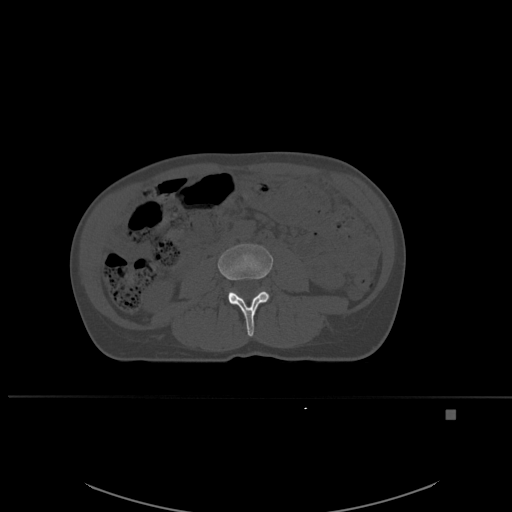
CT including the spine, one axial slice; slice 208 of 537 in the series (ordered by position); bone window (W 1800 / L 400 HU); 1.5 mm slice thickness; 512 × 512 image matrix, field of view 440 × 440 mm. Patient: female, 45 years. From the clinical record (not read from this slice): primary cancer: lung.
Annotated regions visible in this slice (semi-automatic segmentation, software-assisted and operator-edited):
- L3 vertebra: bounding box [x1, y1, x2, y2] px = [218, 244, 273, 337]
- L4 vertebra: [228, 291, 233, 298]